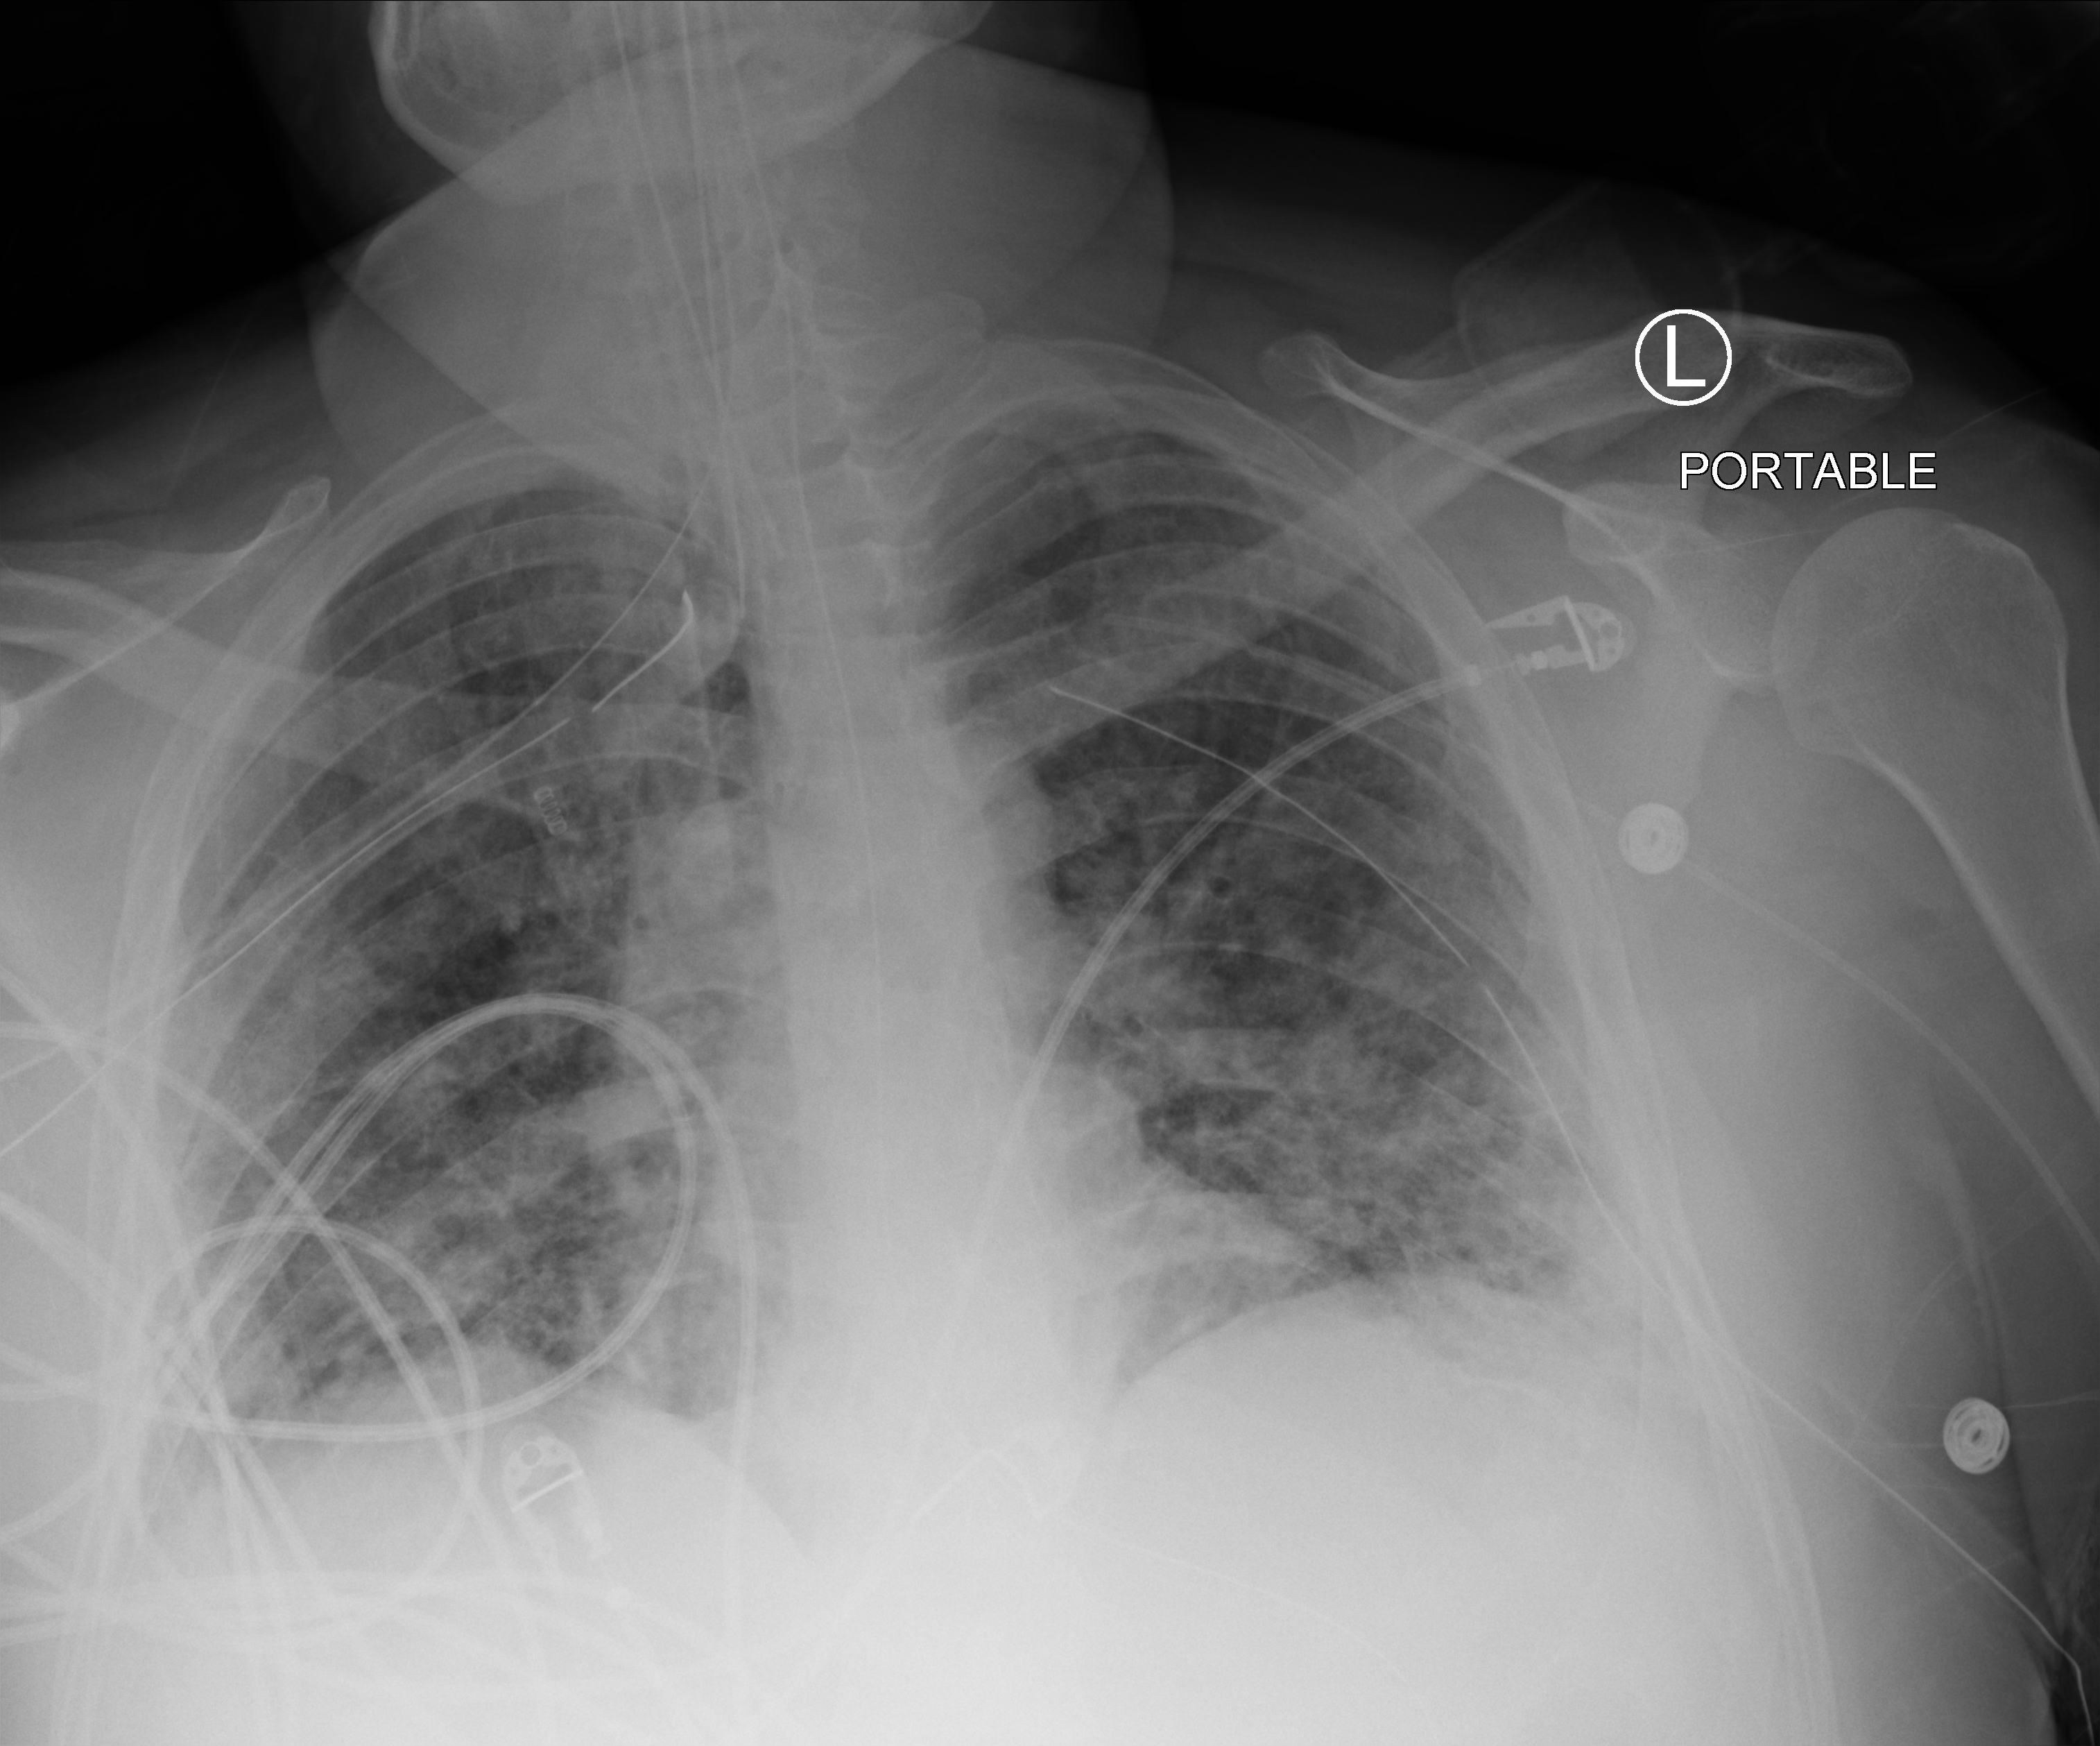
Chest X-ray (portable); anteroposterior (AP) projection. Male patient hospitalised with COVID-19, age 18–59 years.
Hospital-stay facts (about this admission, not read from this image; timing relative to this image not recorded):
- smoking status (admission record): never
- mechanically ventilated during this hospital stay: yes
- admitted to intensive care during this hospital stay: yes